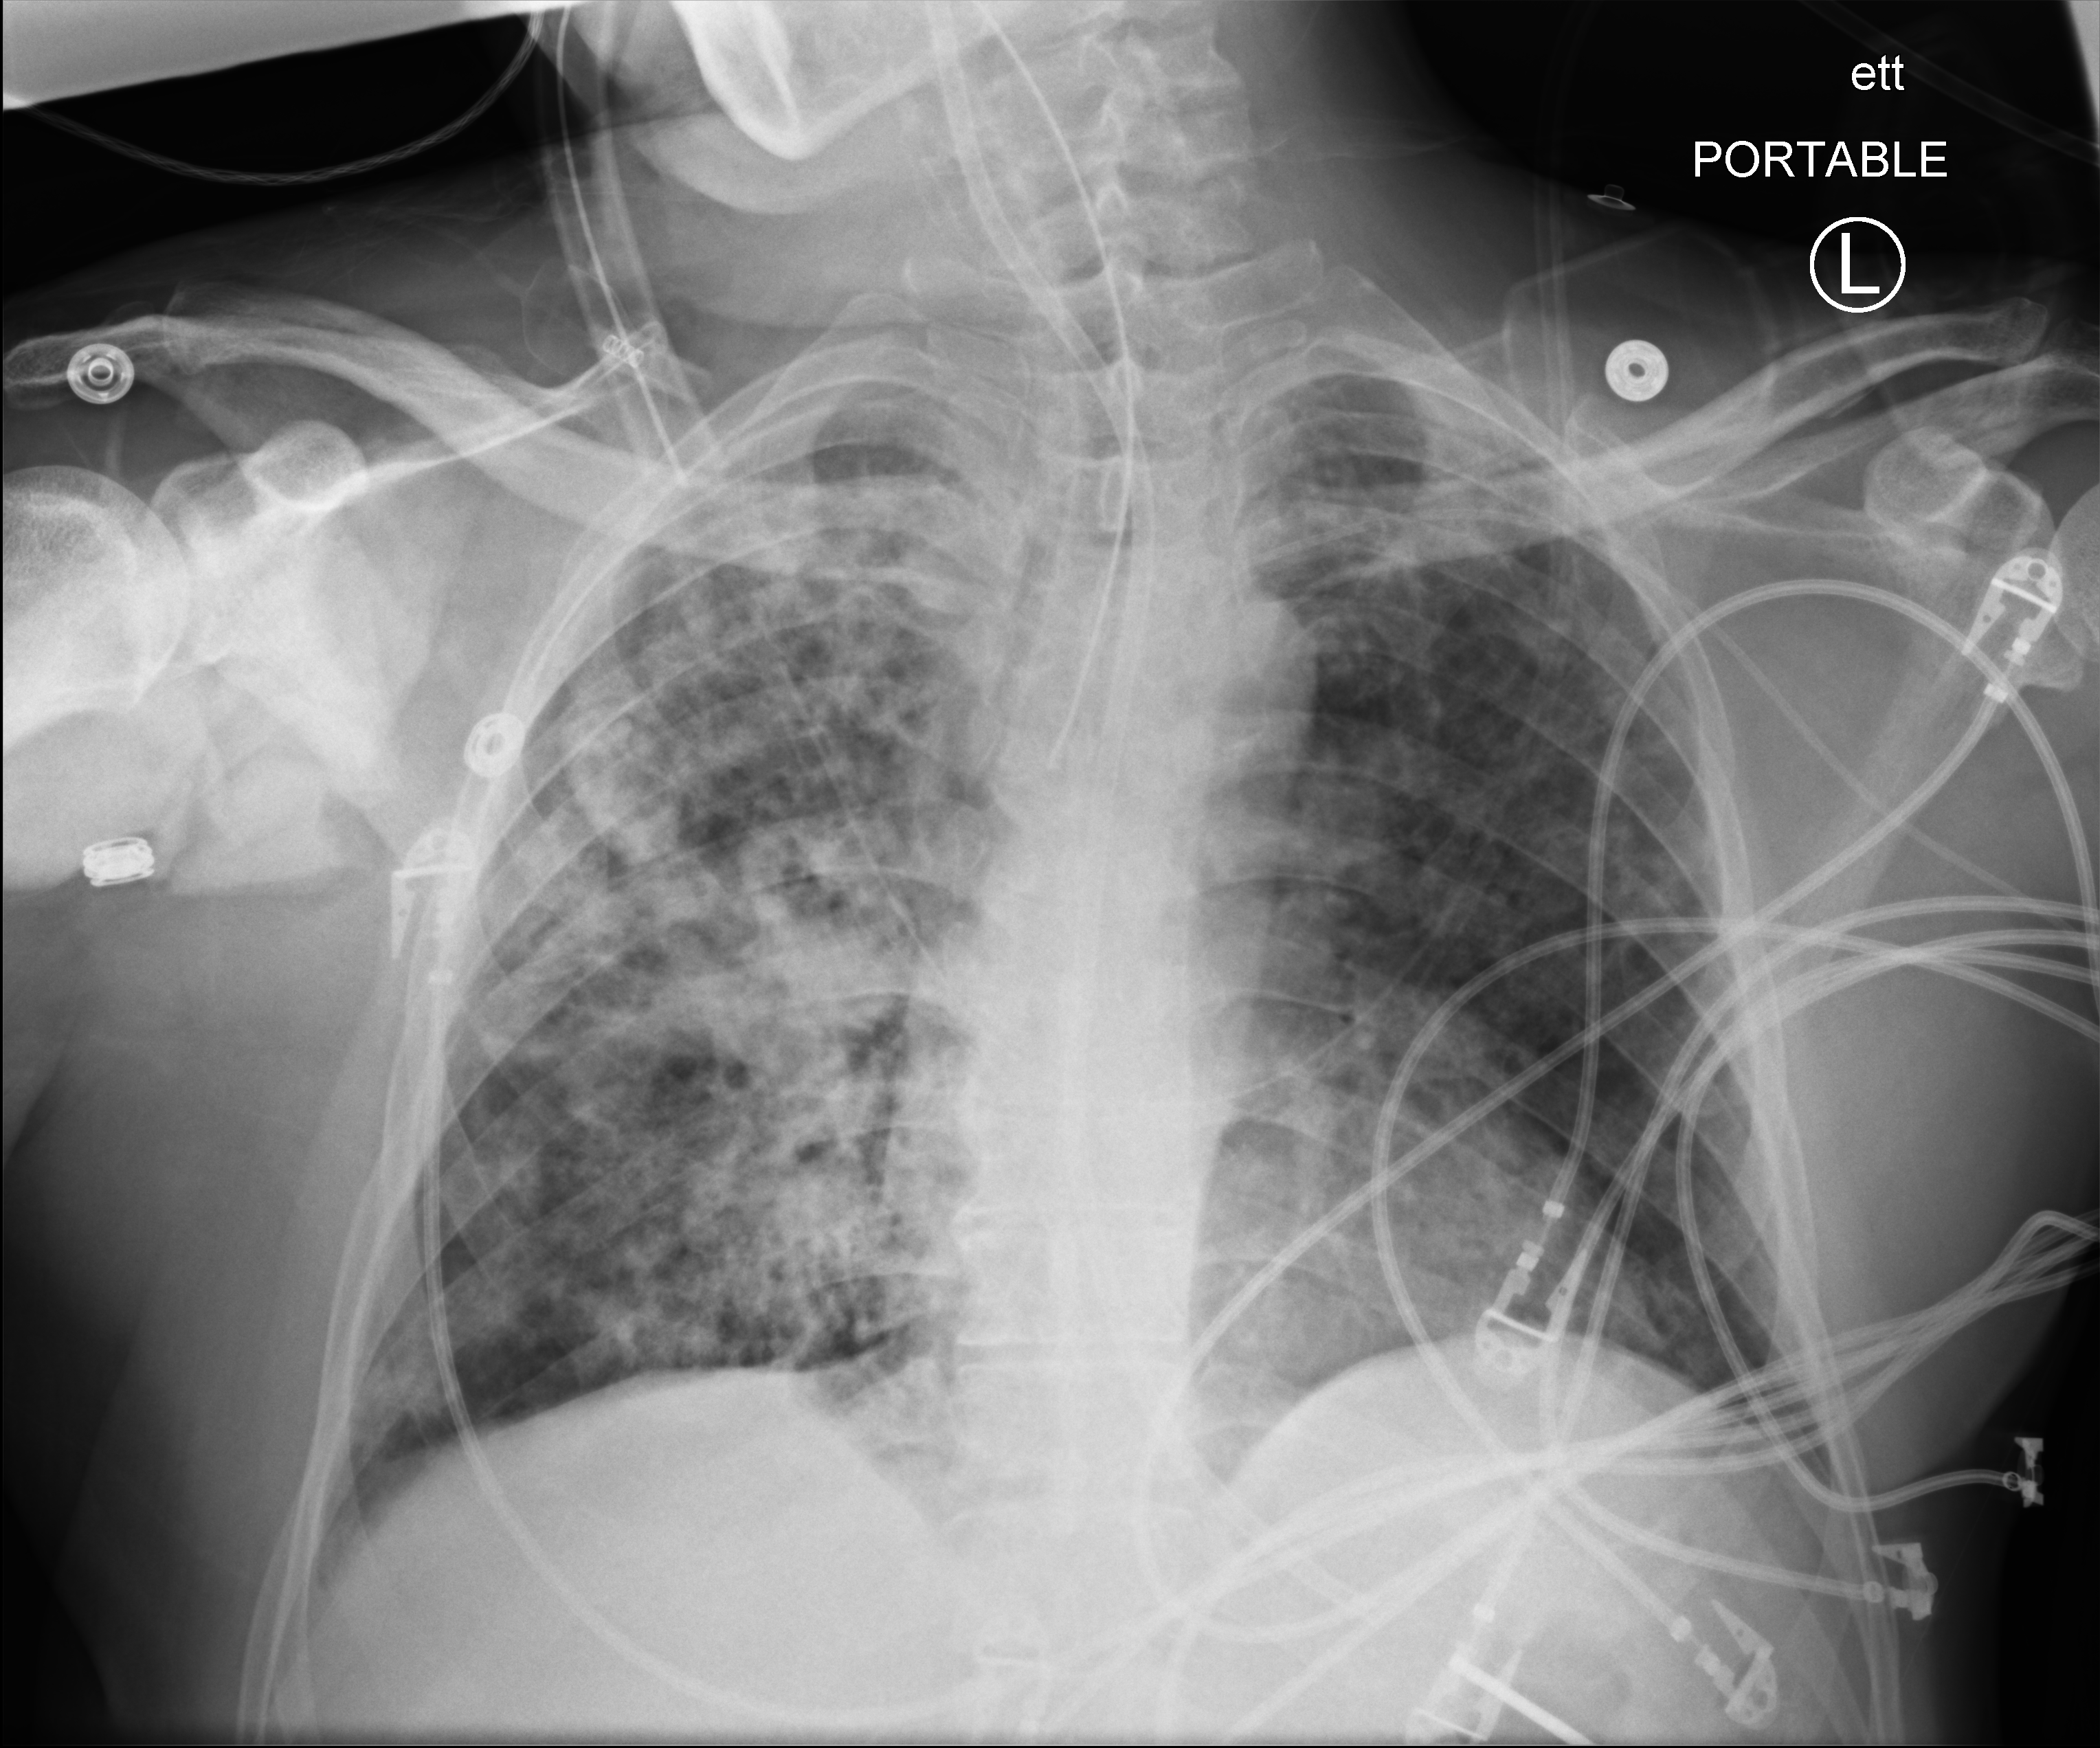
Chest X-ray (portable), anteroposterior (AP) projection. Male patient hospitalised with COVID-19, age 18–59 years.
Hospital-stay facts (about this admission, not read from this image; timing relative to this image not recorded): other chronic lung disease (admission record): no; mechanically ventilated during this hospital stay: yes.